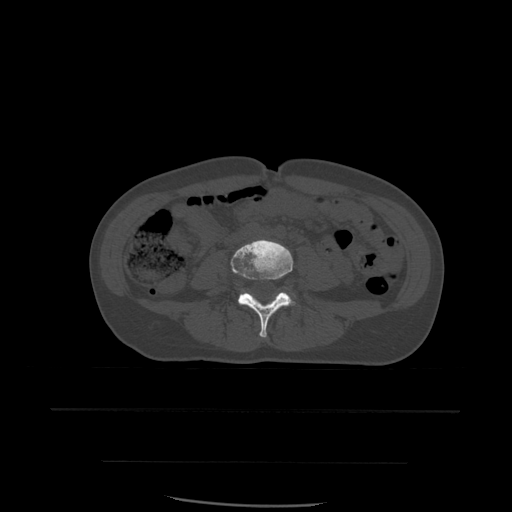
CT including the spine, one axial slice. Position 168 of 574 along the scan axis. Bone window (W 1800 / L 400 HU). 512 × 512 image matrix, field of view 392 × 392 mm. Patient age 48 years. From the clinical record (not read from this slice): primary cancer: lung; vertebrae with lytic lesions (as recorded): T11.
Outlined on this slice (semi-automatic segmentation, software-assisted and operator-edited):
- L4 vertebra: bounding box [x1, y1, x2, y2] px = [231, 240, 294, 338]
- L5 vertebra: [239, 291, 290, 299]